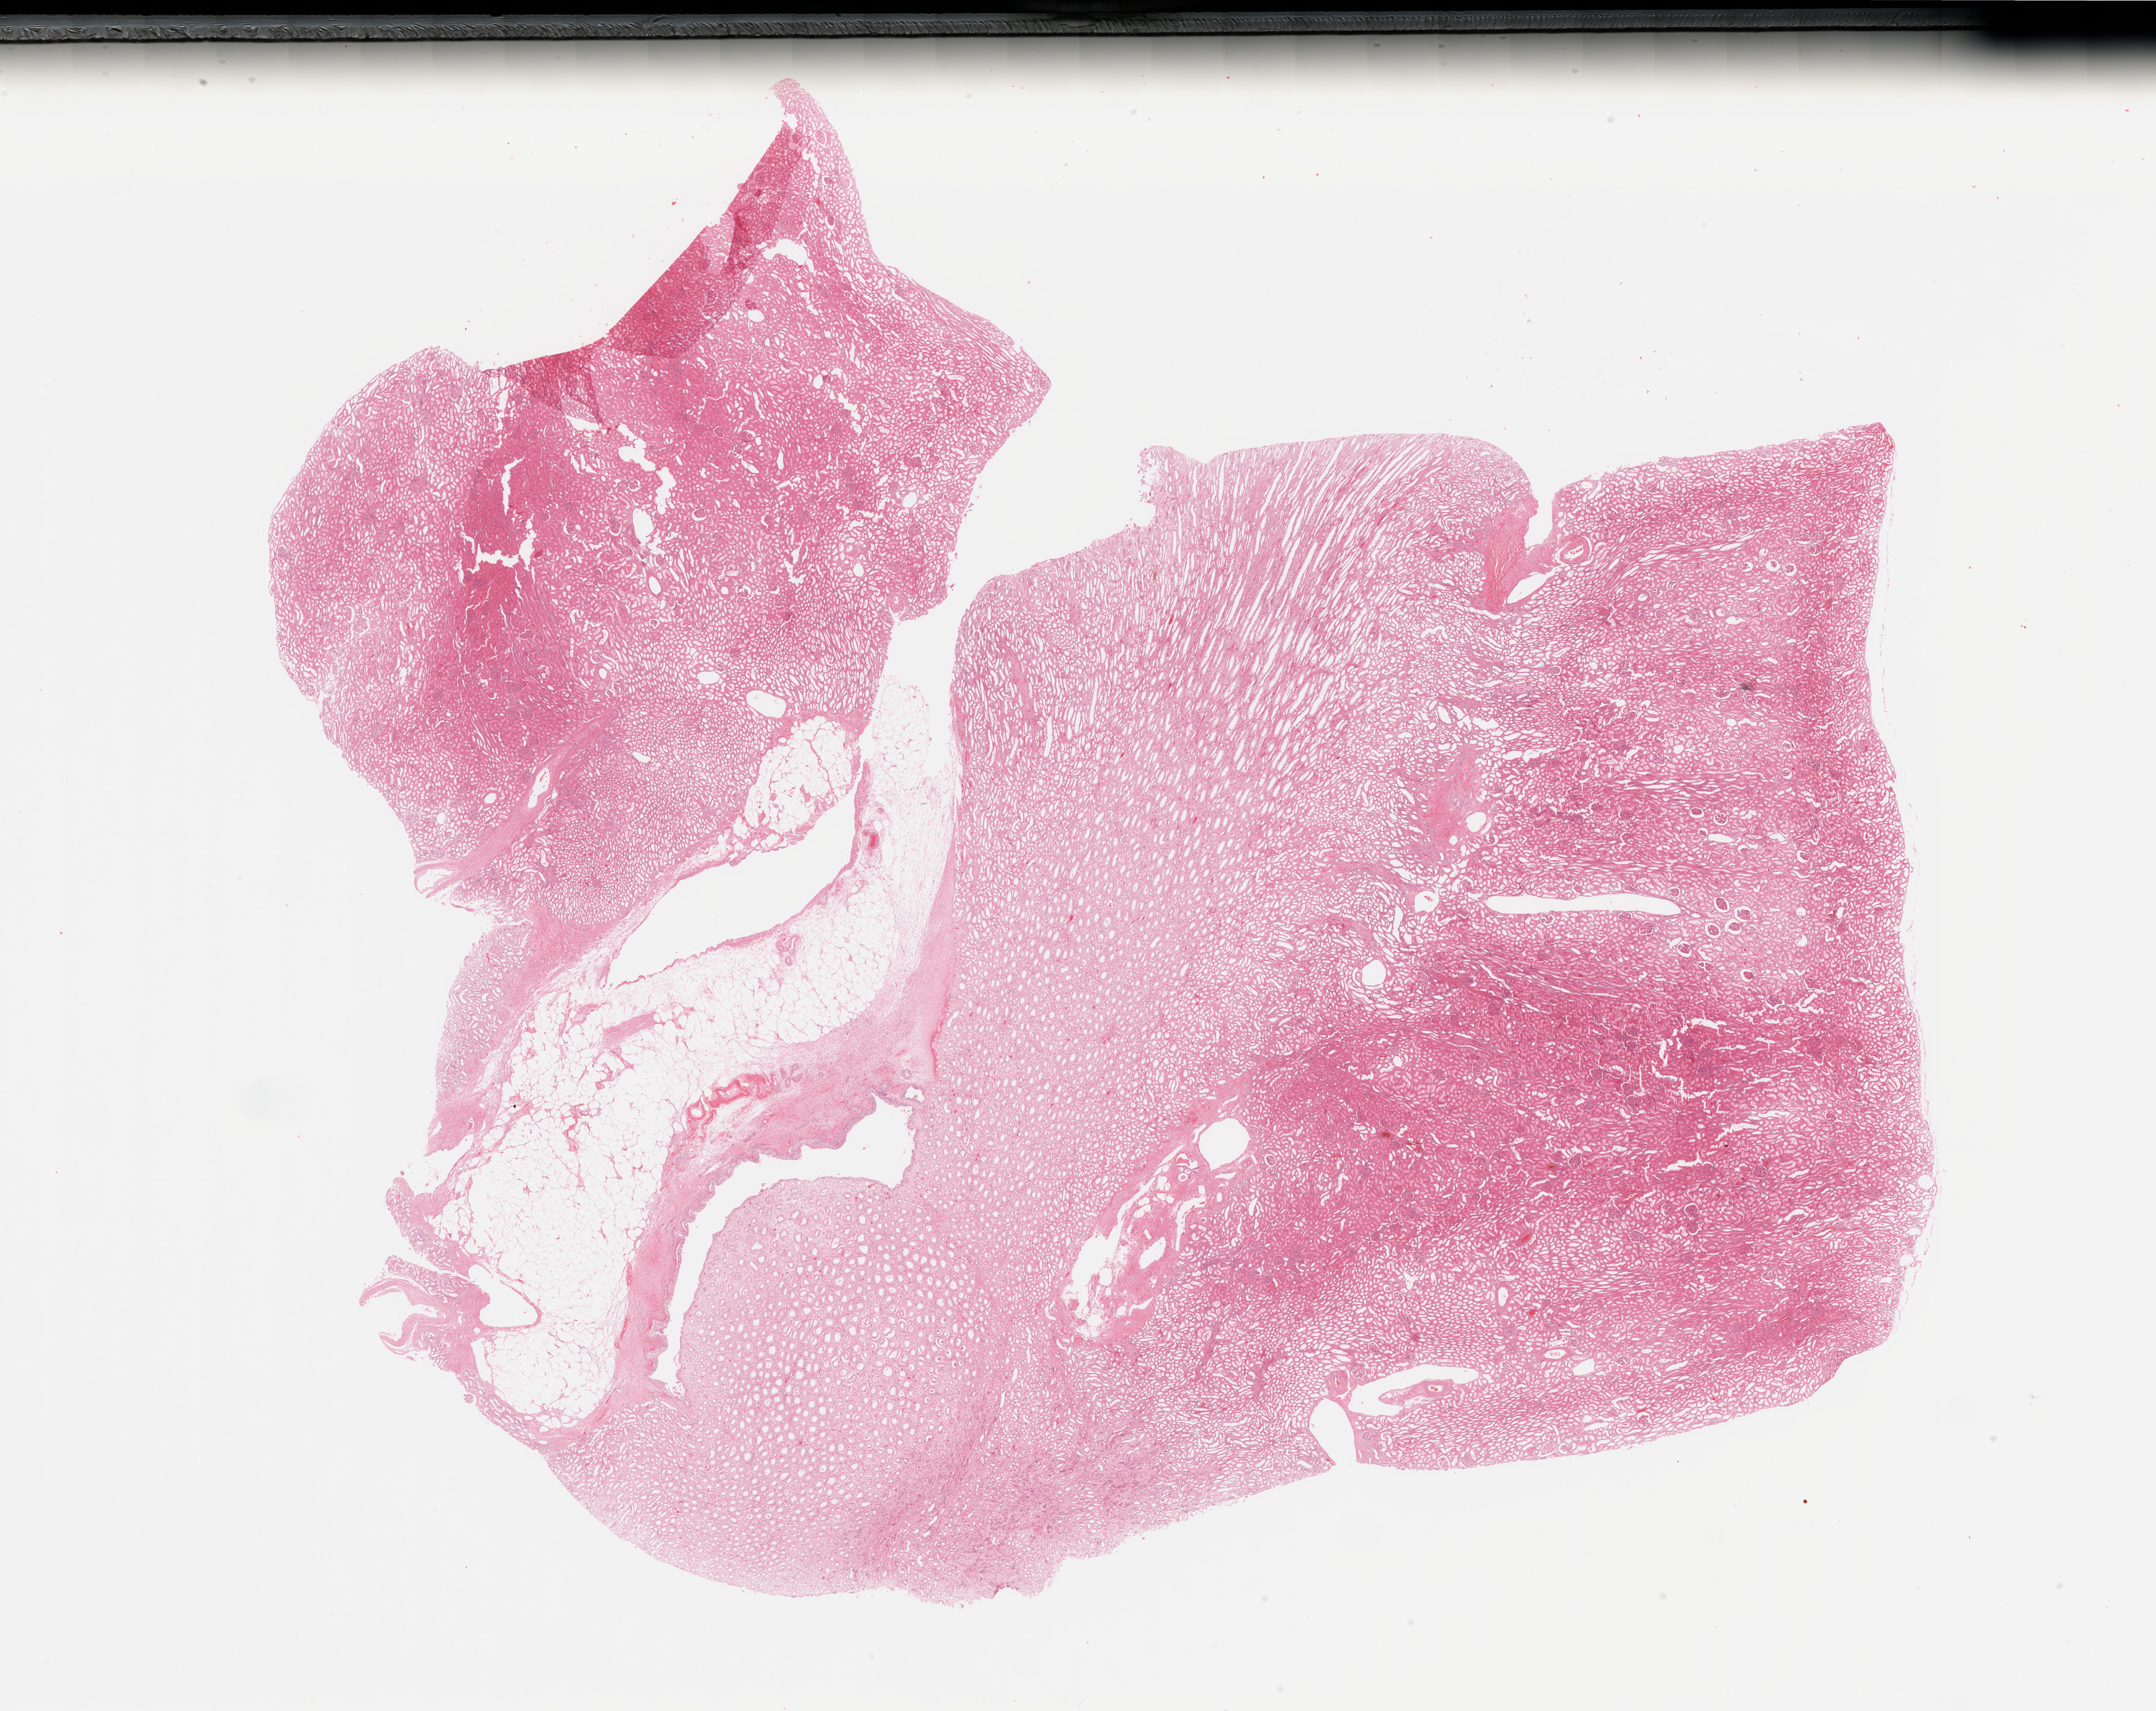
Whole-slide histology image, H&E-stained — low-resolution overview of the scanned area, about 29.5 x 23.4 mm (acquisition: 20x scan), normal (non-tumour) tissue sample, sampled site: kidney. 41-year-old female patient.
This section: normal (non-tumour) tissue from the same patient. Patient diagnosis: Renal cell carcinoma, NOS.